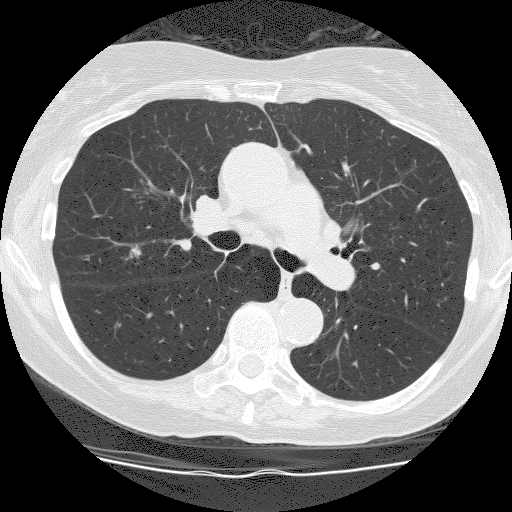
Low-dose screening chest CT, axial slice. Second screening round (one year after baseline). Lung window (W 1500 / L -600 HU). 2.5 mm slice thickness. Slice 71 of 186 in the series. 512 × 512 image matrix. Female, age 66 years at enrolment.
• Expert-annotated lung lesion, bounding box [x1, y1, x2, y2] px = [106, 230, 158, 278].
• The screening reader recorded 2 non-calcified nodules or masses ≥4 mm on this exam; which of them this box marks is not recorded.
• Lung cancer was diagnosed 209 days after this screen: squamous cell carcinoma, NOS, right upper lobe, stage IIIA (AJCC 6th edition), 10 mm at pathology.